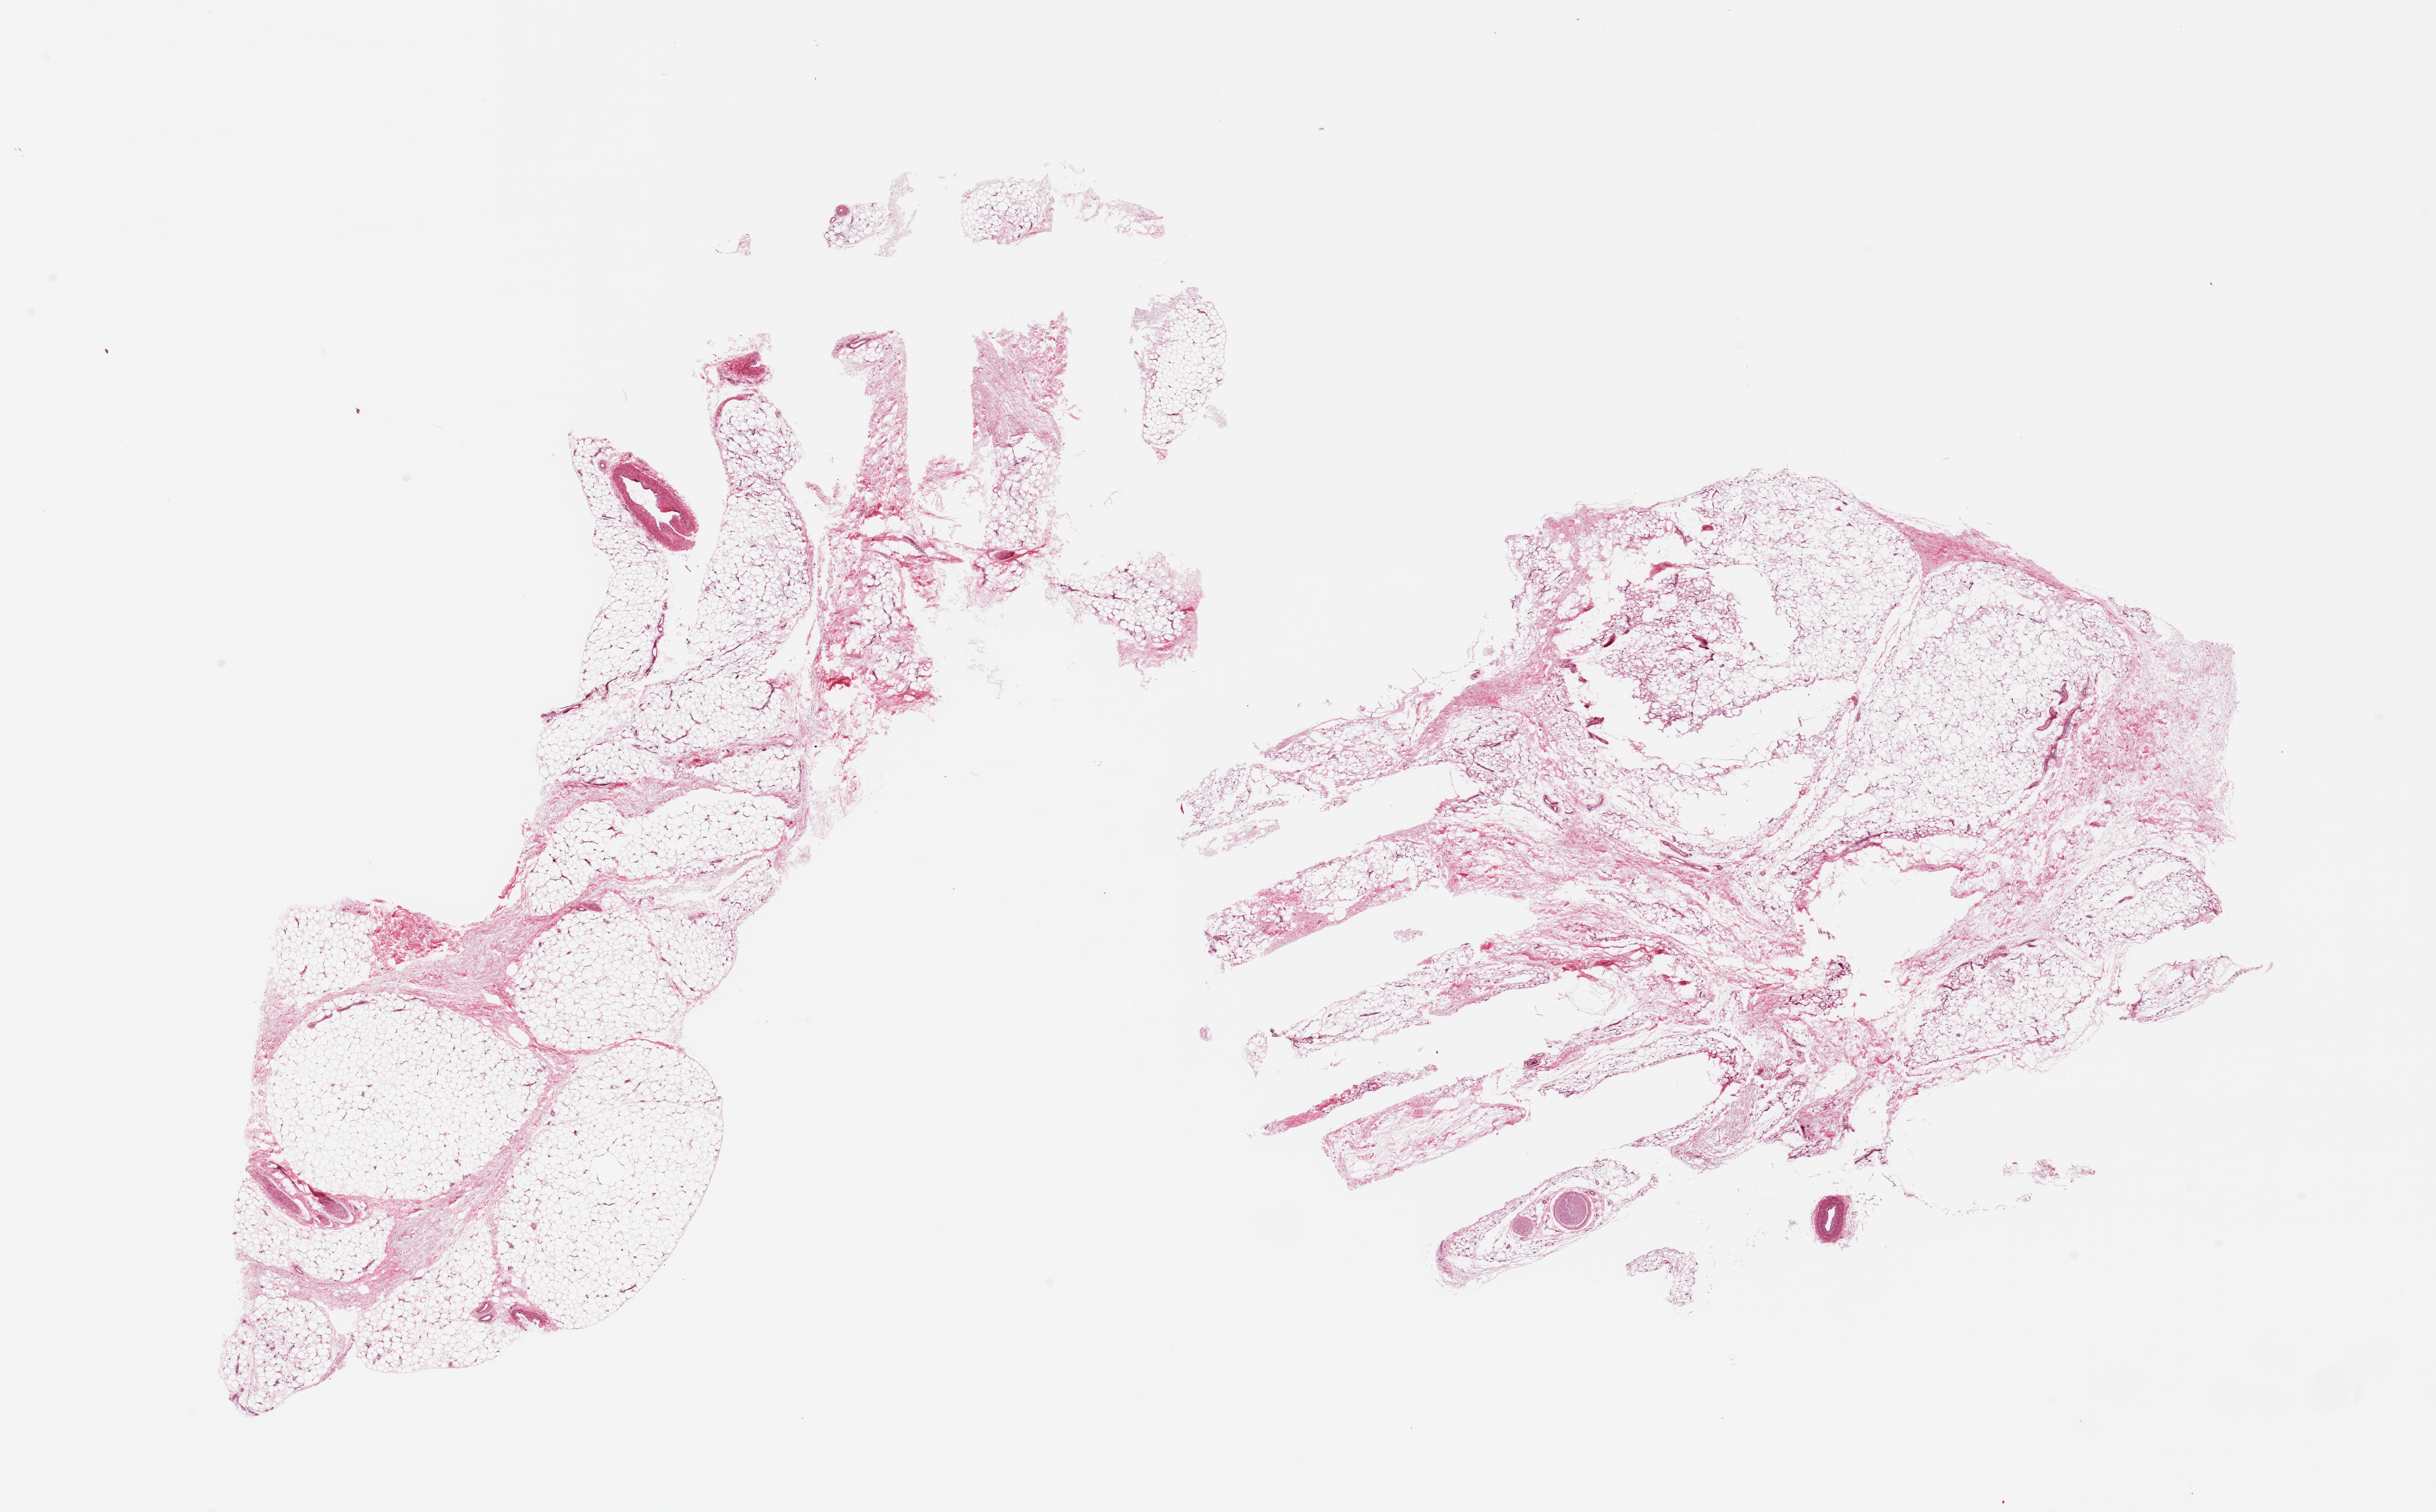
Whole-slide image, H&E stain, brightfield, low-resolution overview of the scanned area, about 28.5 x 17.7 mm (slide scanned at 20x), PAXgene-fixed, paraffin-embedded tissue, target tissue: adipose tissue, donor tissue sample. Donor sex: male.
Pathologist's review note for this sample: 2 pieces, ~5-10% fascia.